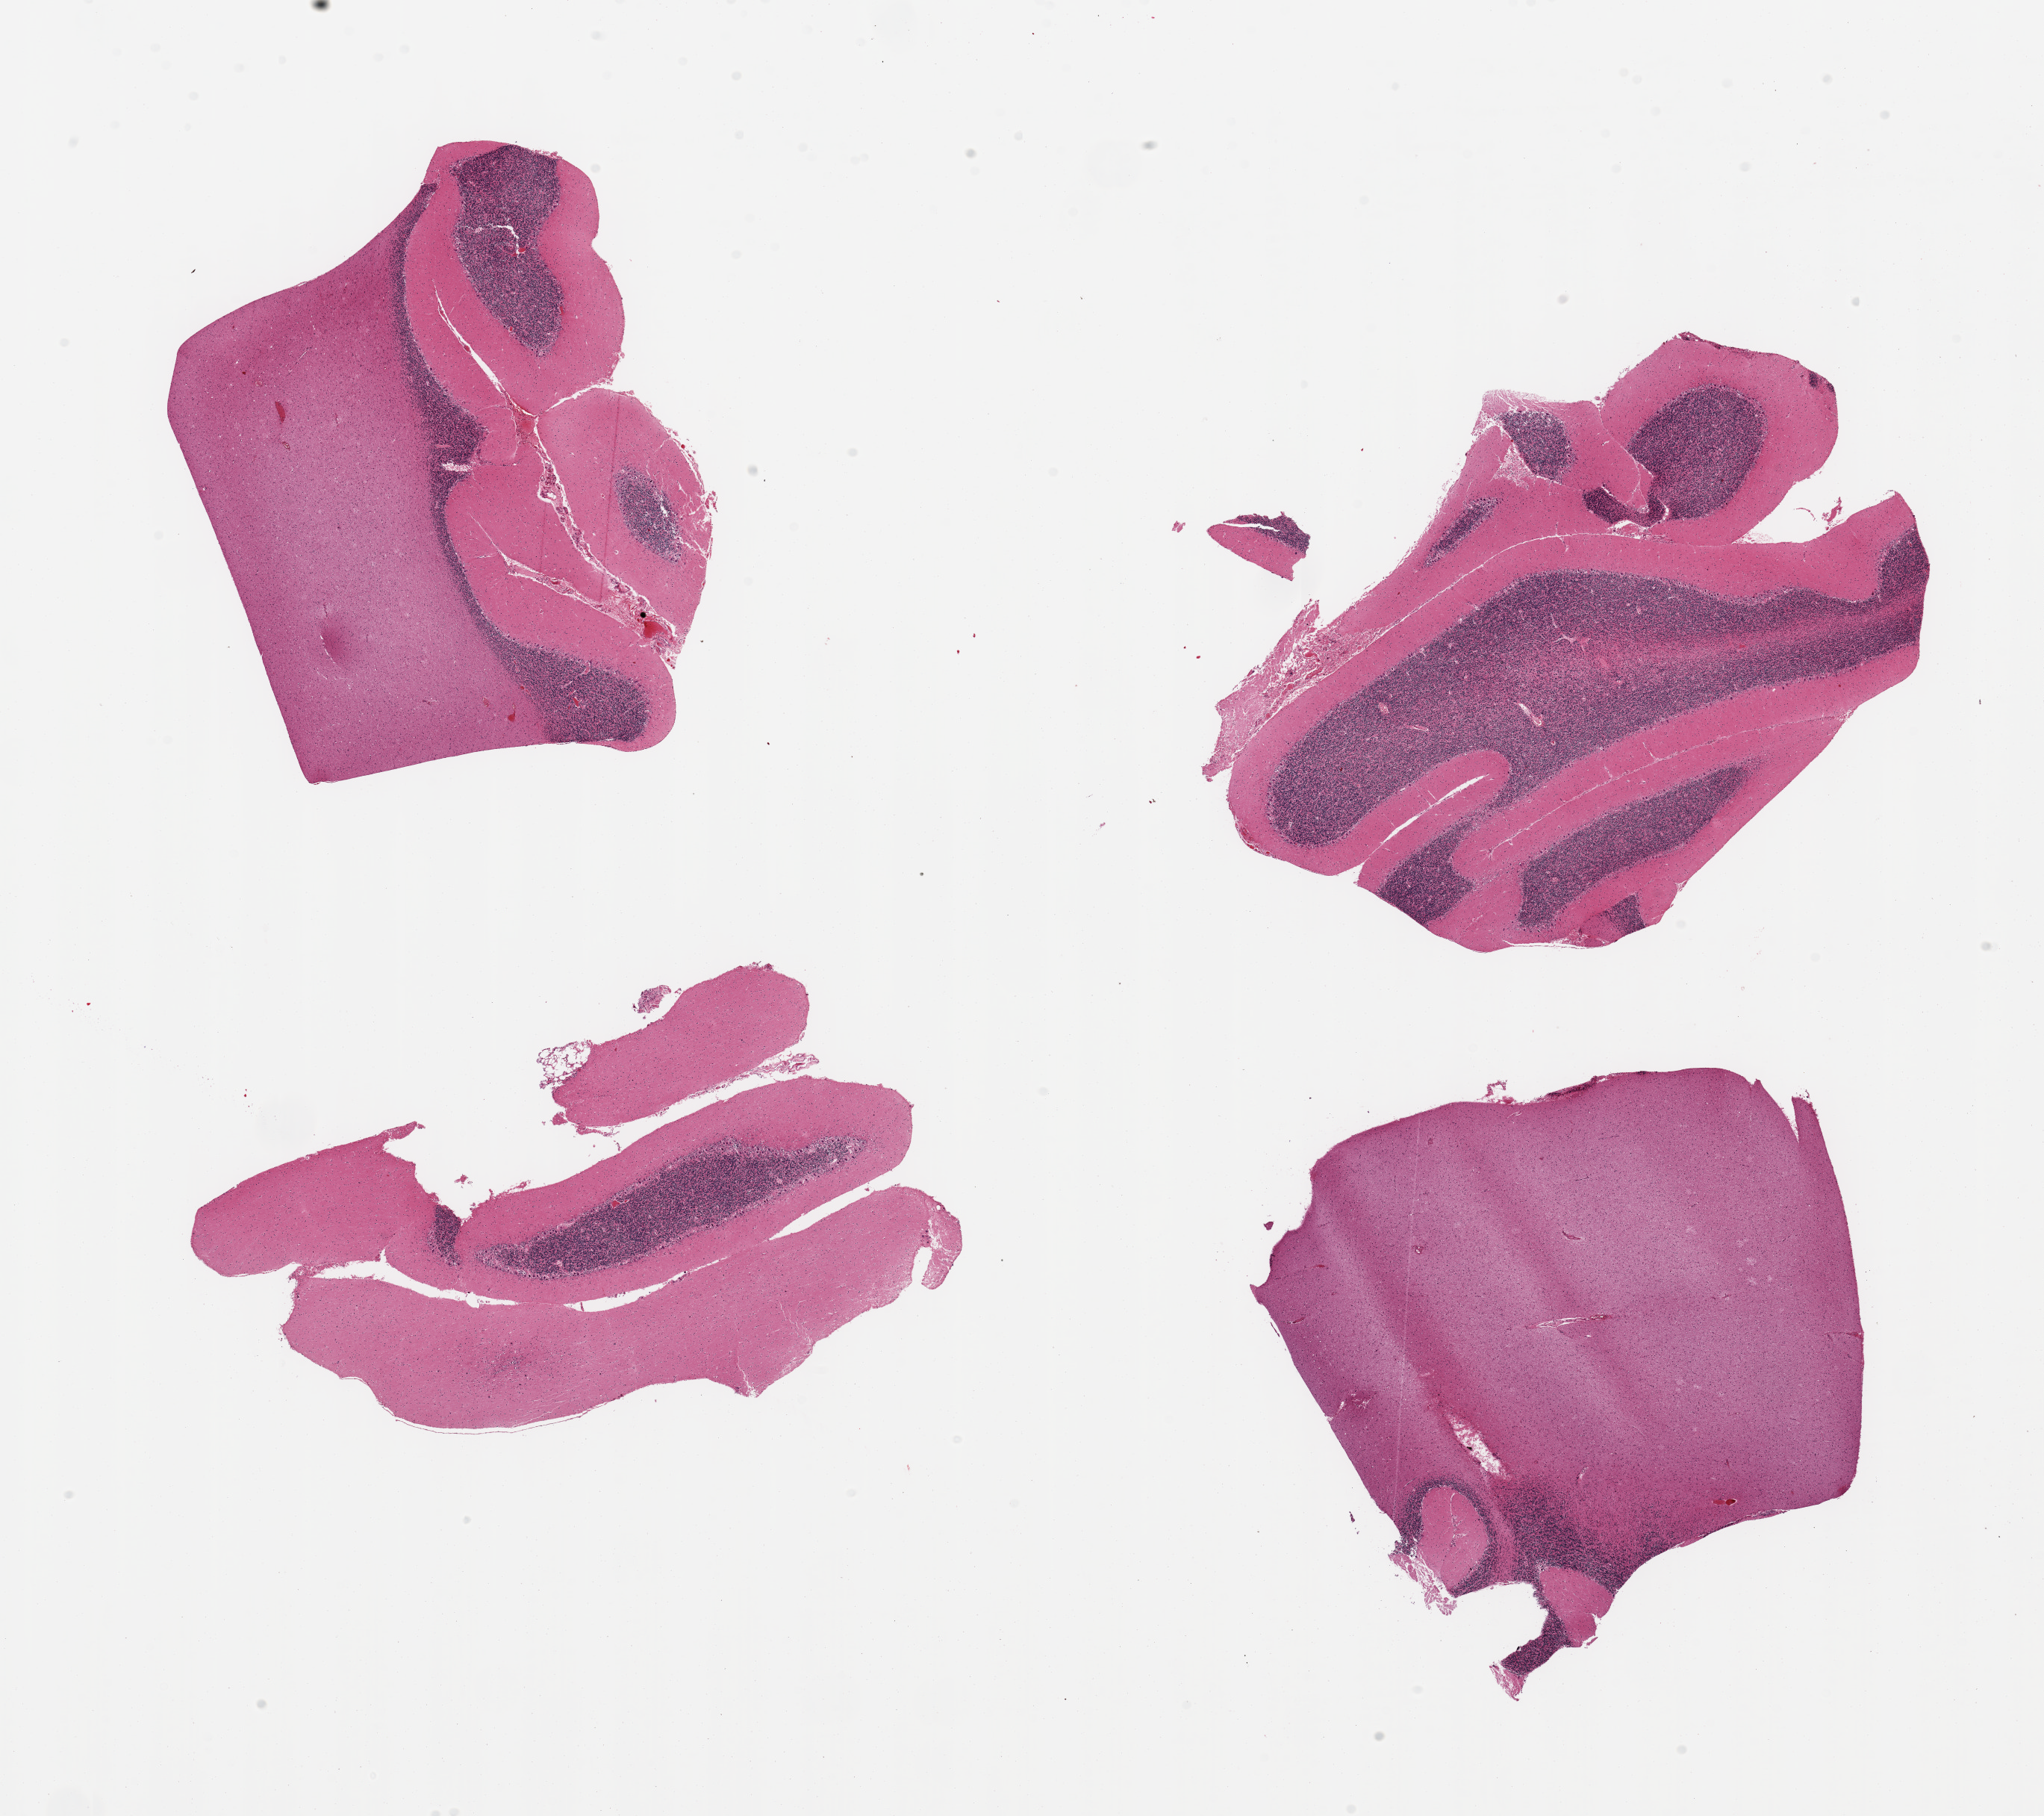
Haematoxylin and eosin whole-slide image, brightfield — a low-resolution overview of the entire scanned area, about 21.7 x 19.2 mm. PAXgene-fixed, paraffin-embedded tissue. Section of cerebellum (target tissue). Tissue donor sample. Donor: male.
• review note (as recorded): 4 pieces; small amount of adherent meninges